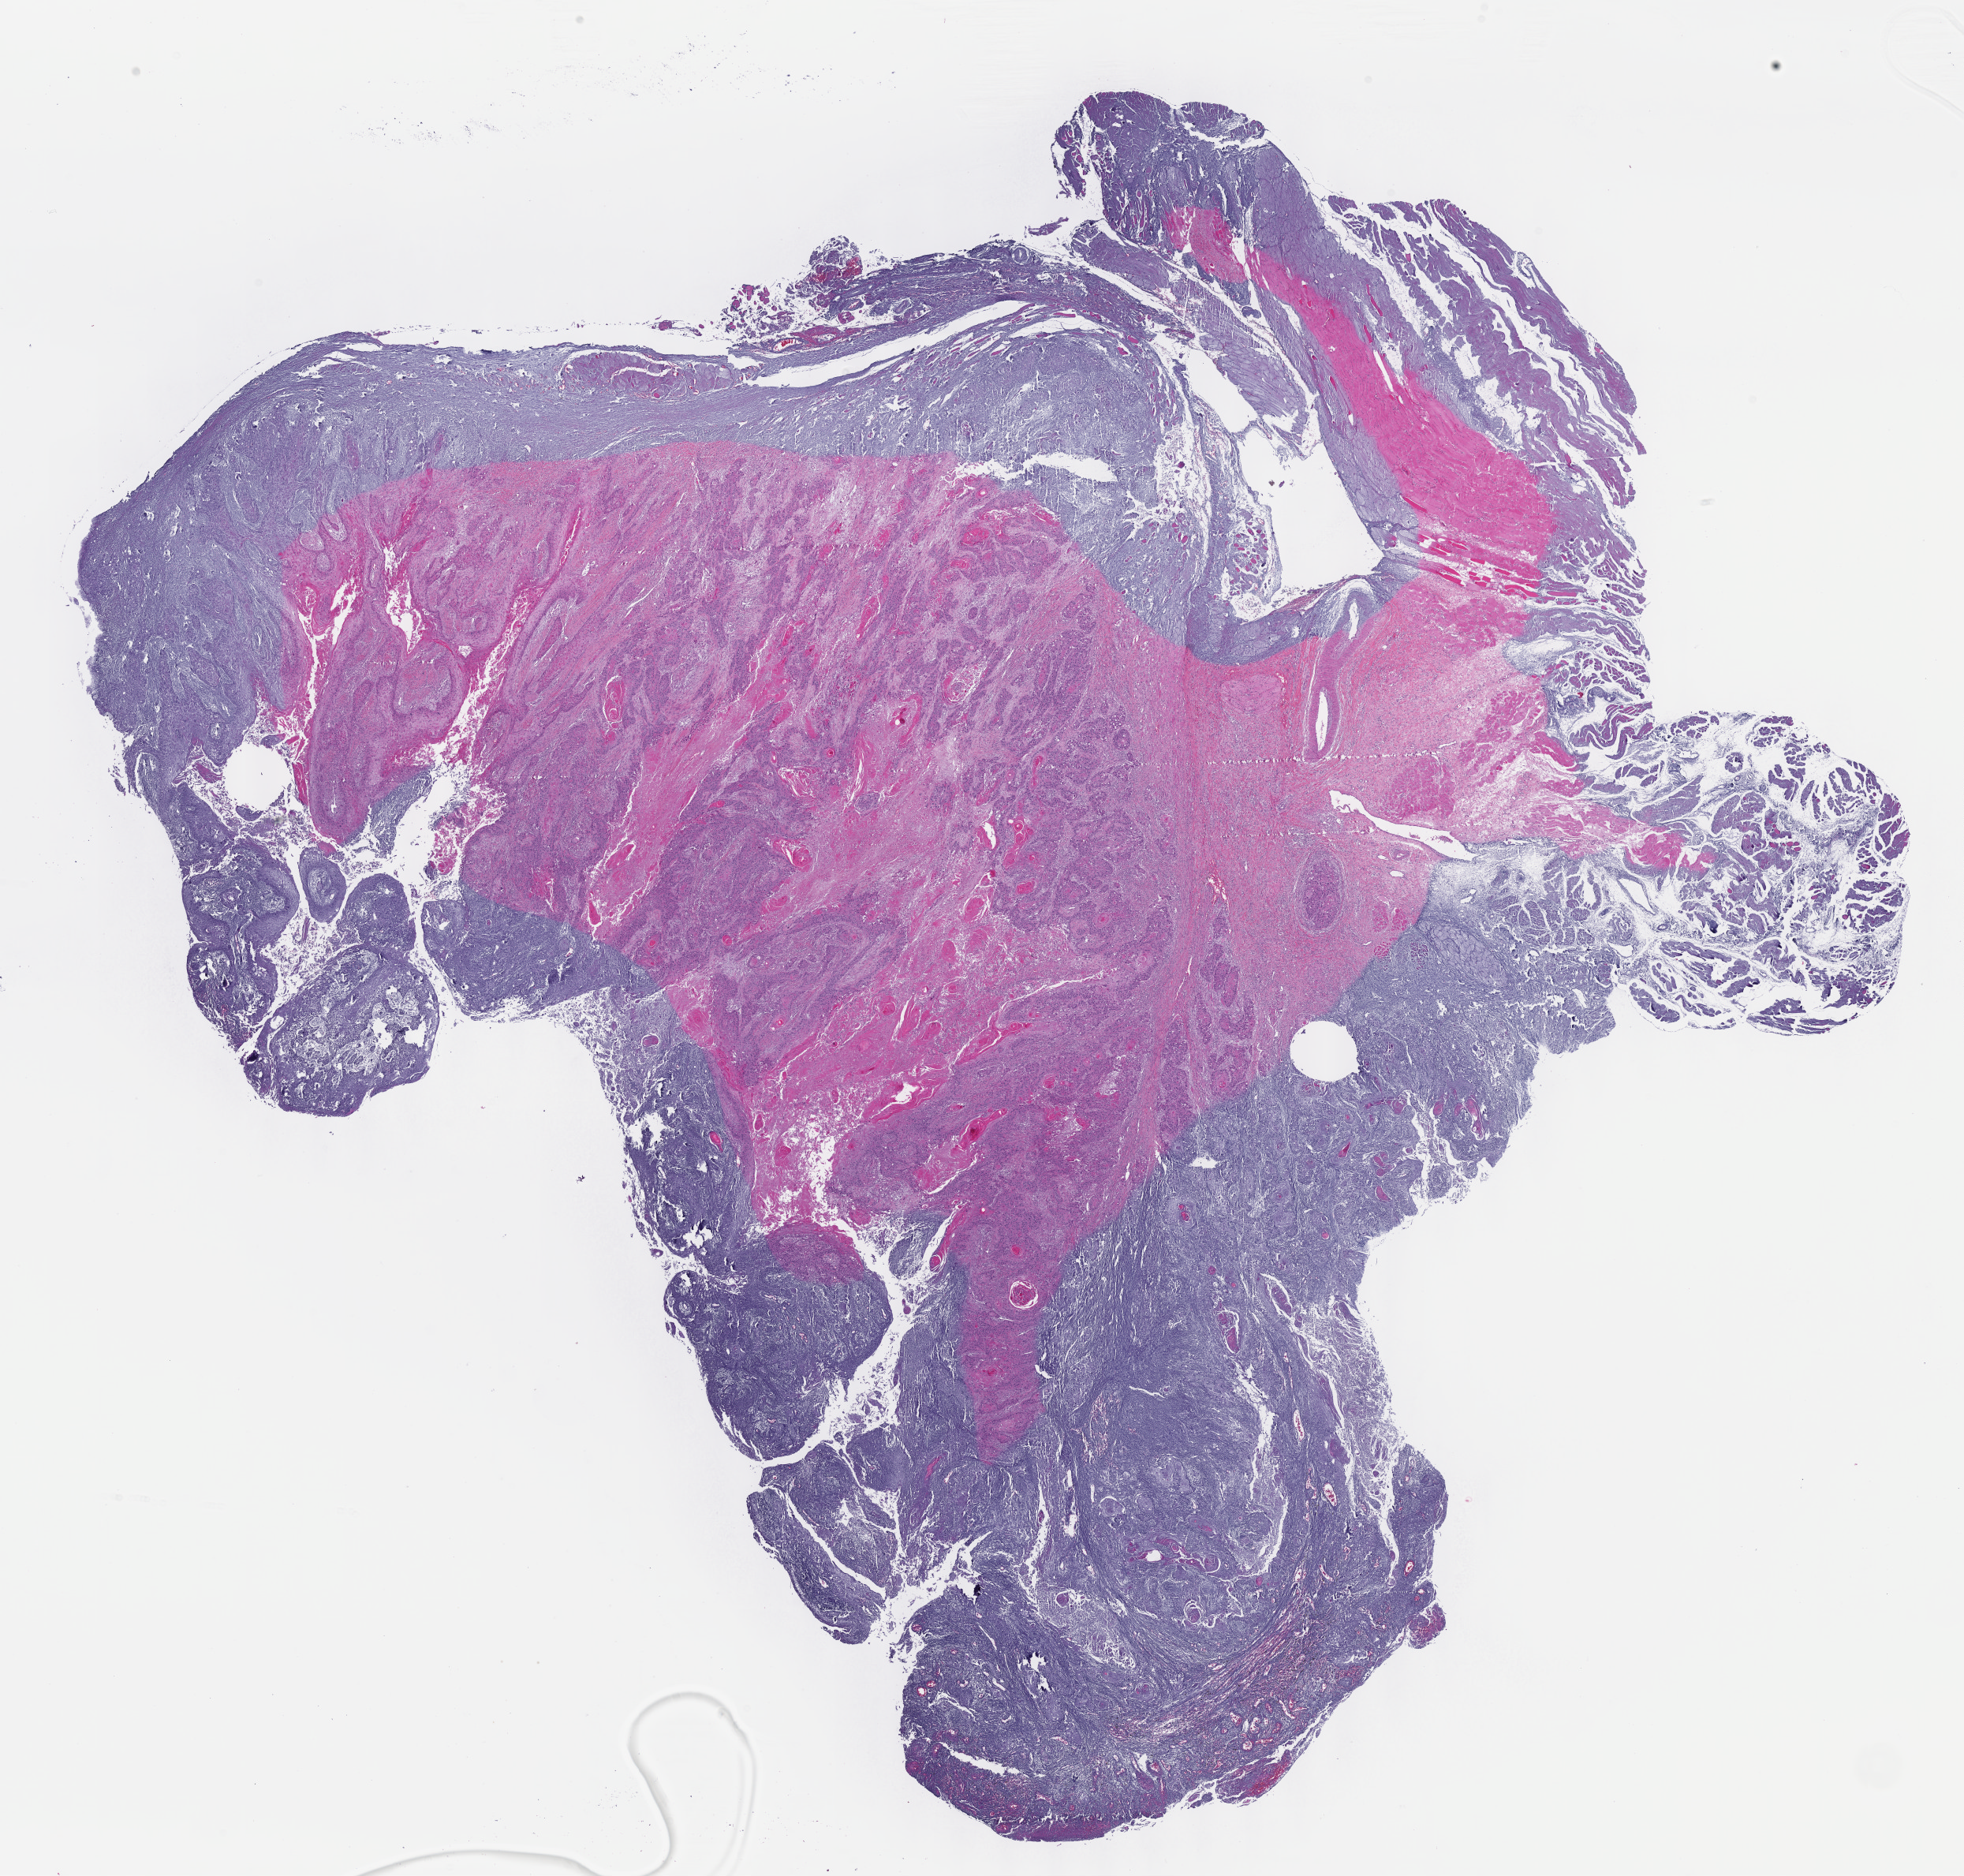
Hematoxylin and eosin (H&E) stained whole-slide image, shown as a low-resolution overview of the whole scanned area (about 20.1 x 19.2 mm, slide scanned at 40x). FFPE section. Head and neck, primary tumour sample. Male patient; age at initial diagnosis 49 years. Histologic grade: G3 (poorly differentiated).
Laterality: right. AJCC pathologic stage: IVA (7th edition). Diagnosis: Squamous cell carcinoma, NOS (larynx, NOS).